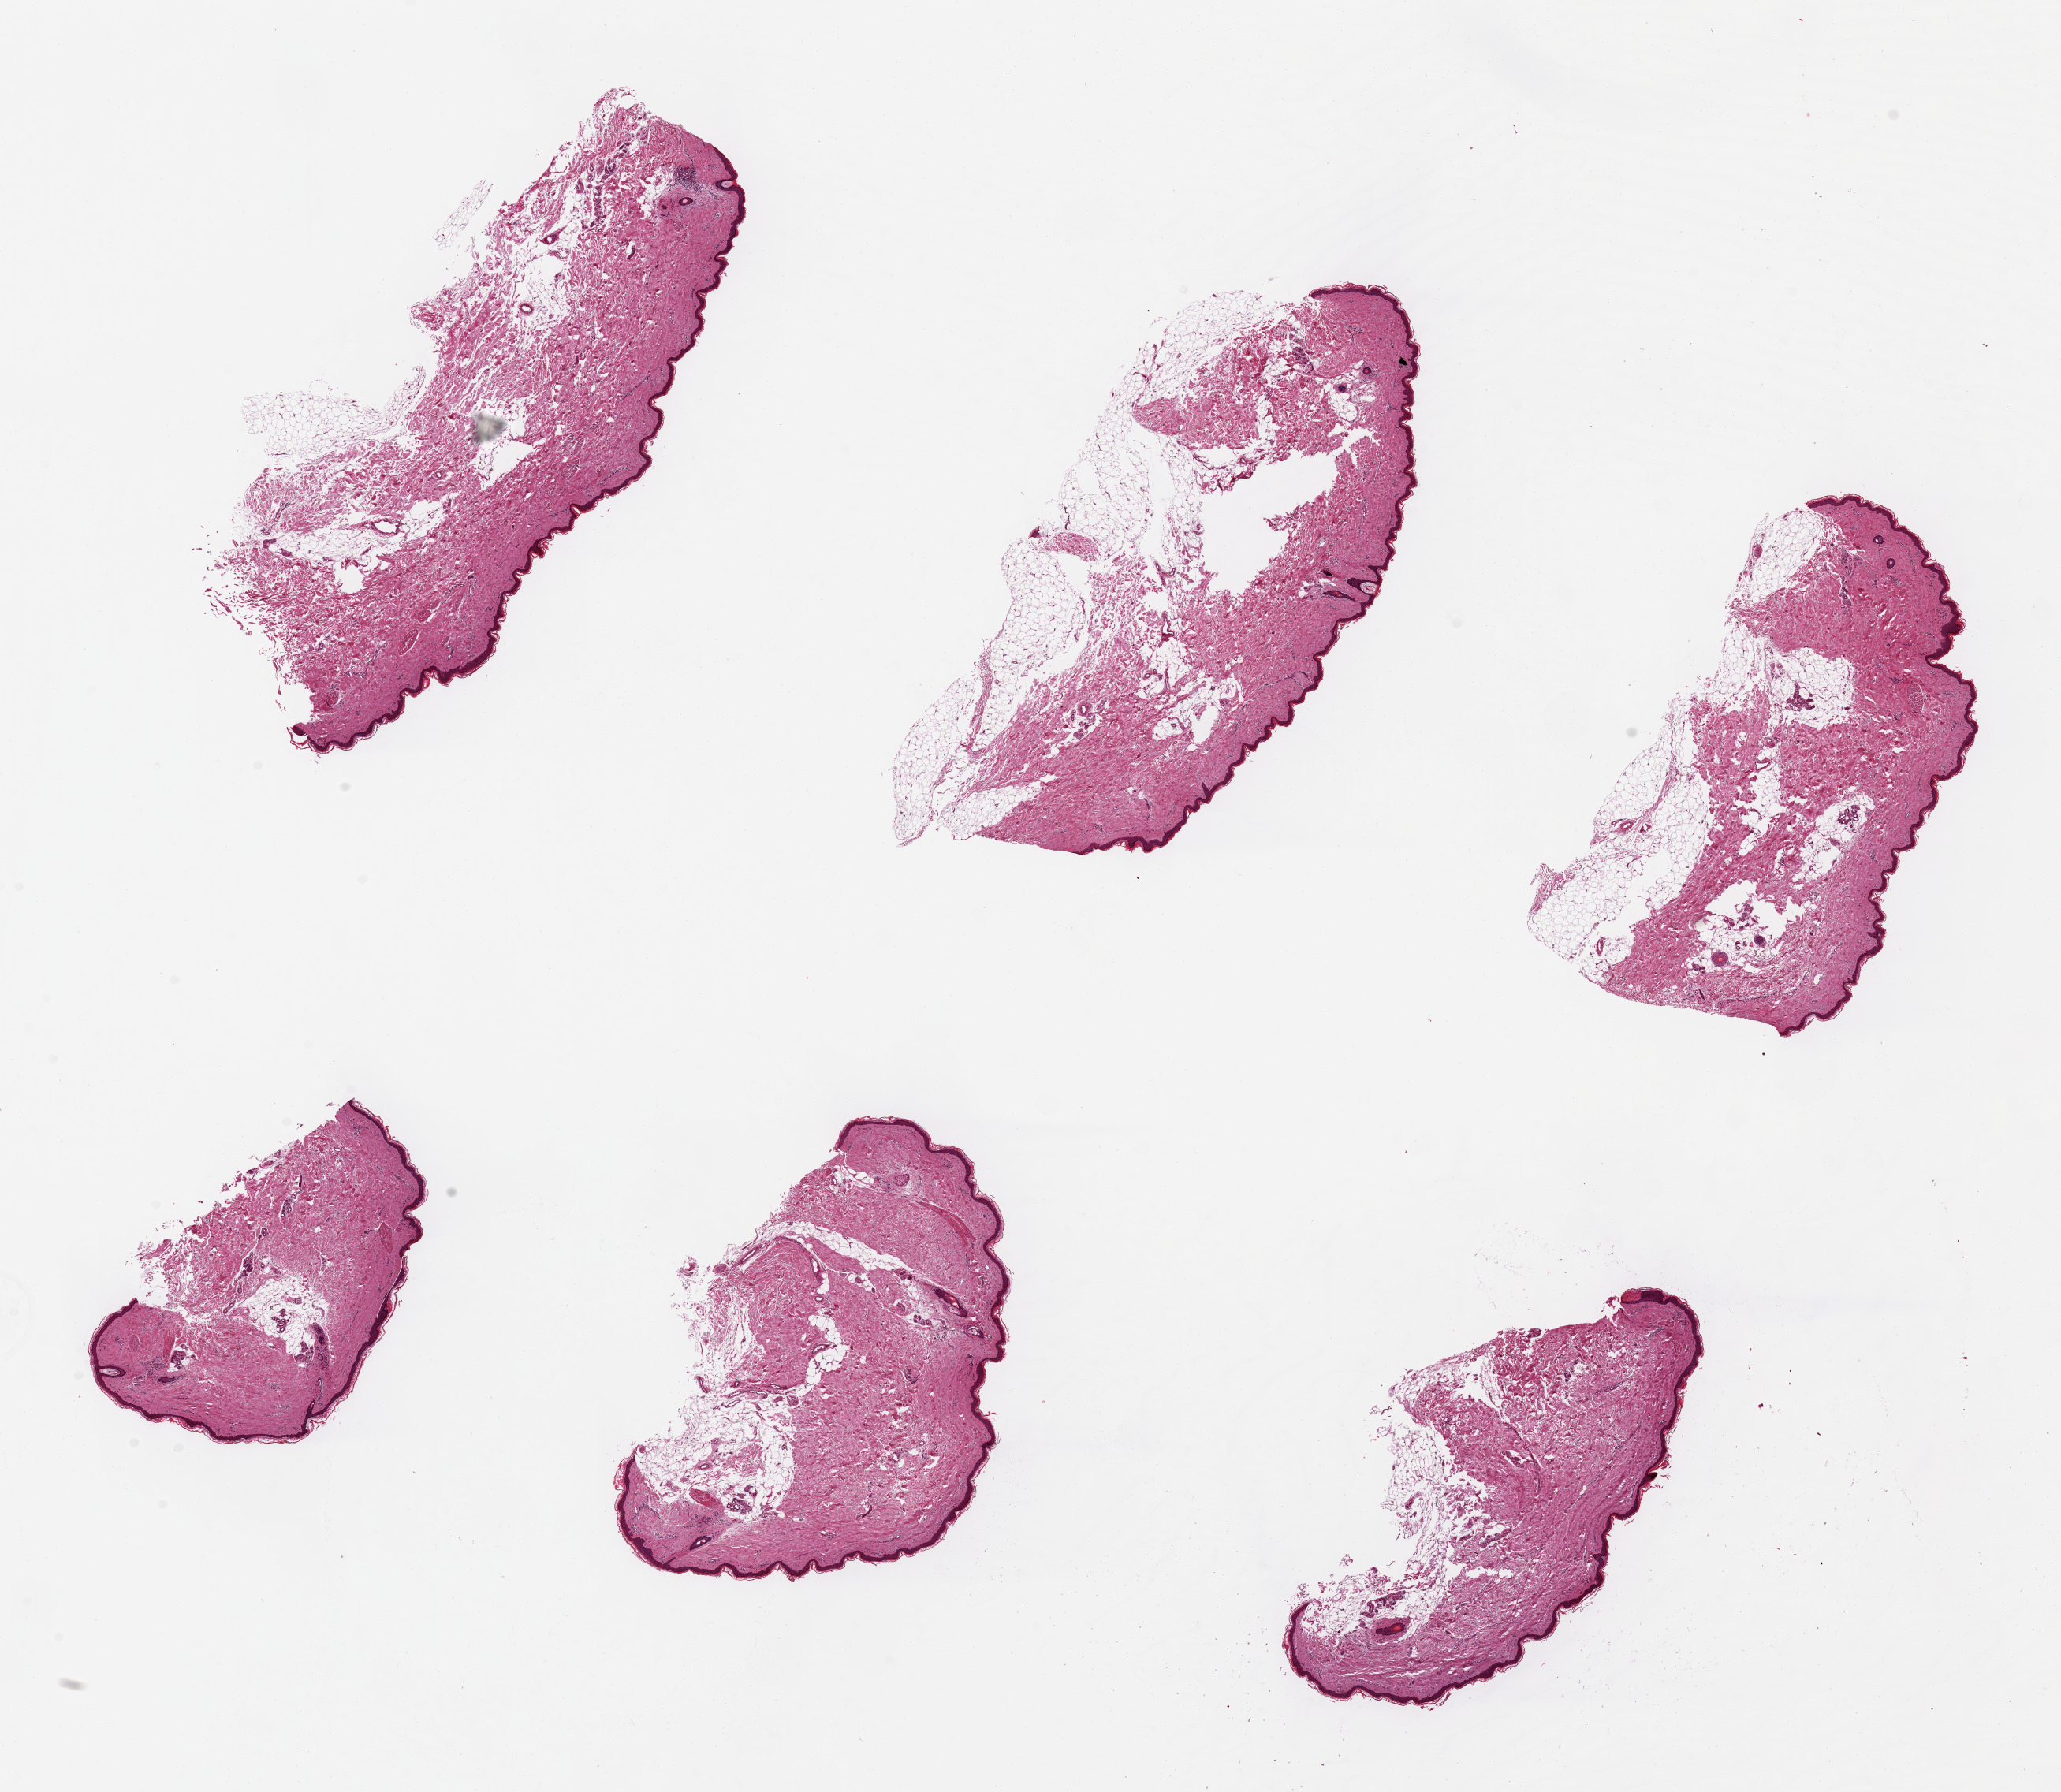
Digitized hematoxylin and eosin (H&E)-stained section, brightfield — whole scanned area (about 20.7 x 18.0 mm, slide scanned at 20x) shown as a low-resolution overview, PAXgene-fixed, paraffin-embedded tissue, section of skin of lower leg (target tissue), donor tissue sample. Donor sex: female.
Review note (as recorded): 6 pieces up to 7x3 mm; up to 1.5 mm subcutaneous adipose in 3 pieces.